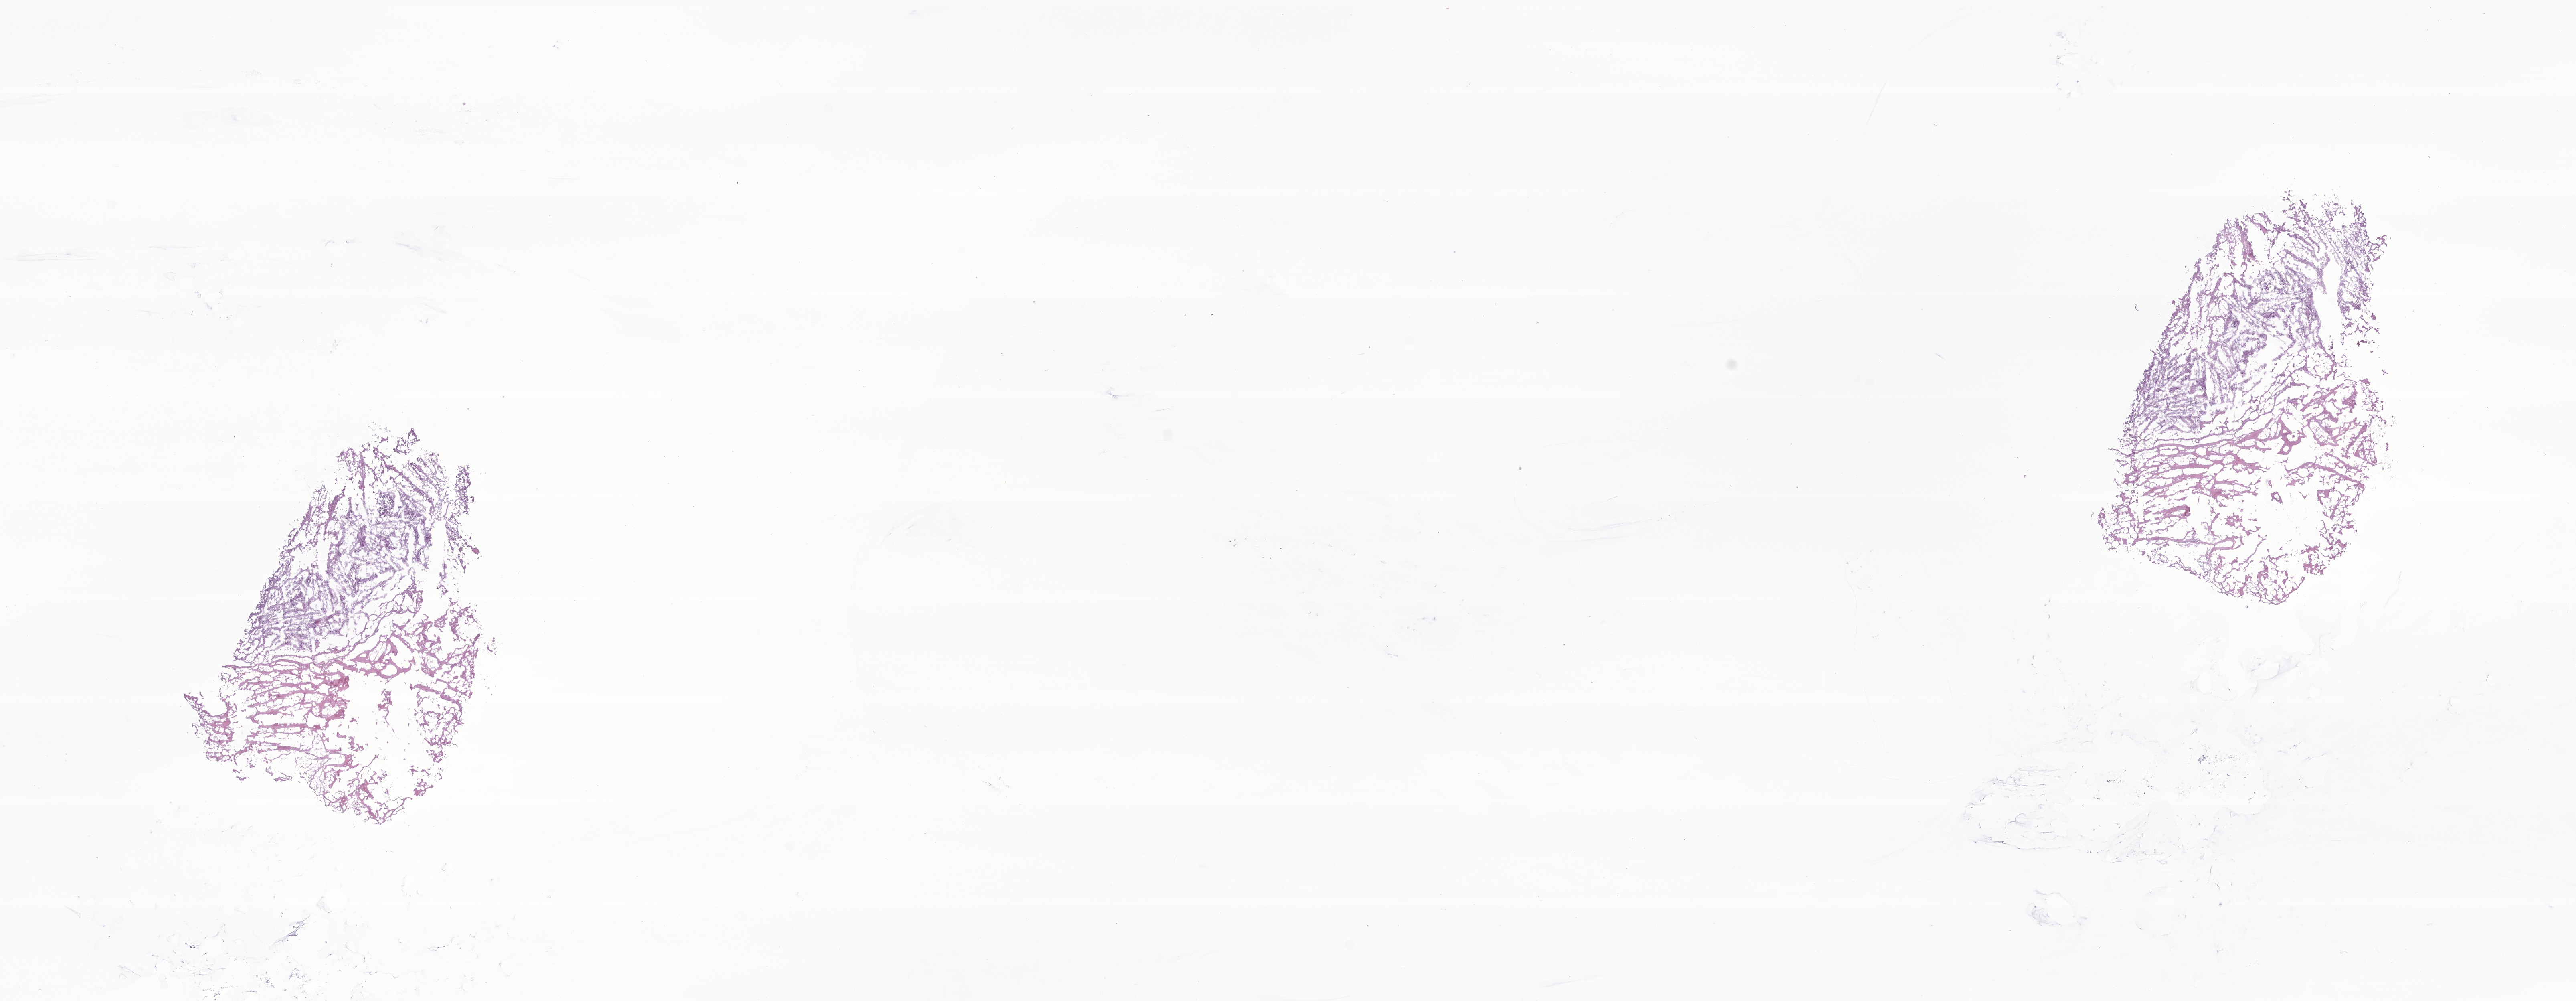
Whole-slide image, H&E stain of tumor tissue from the brain, whole scanned area (about 27.1 x 10.5 mm) shown as a low-resolution overview. Frozen section (OCT-embedded). Male patient, age 104 months (8 years 8 months).
Diagnosis: Neoplasm, uncertain whether benign or malignant.